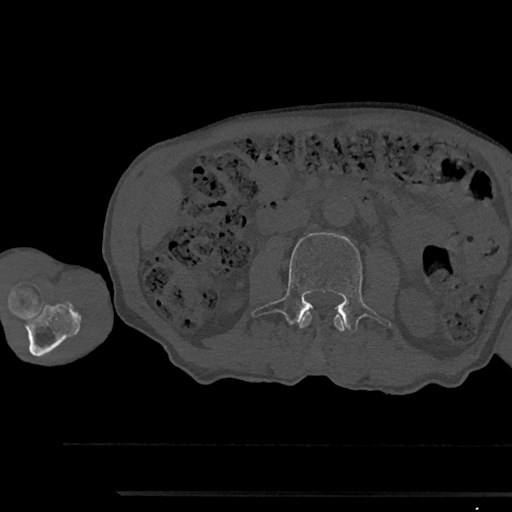
CT including the spine, one axial slice; slice 507 of 797 in the series (ordered by position); reconstruction kernel Br40s/3; bone window (W 1800 / L 400 HU); 0.5 mm slice thickness; 512 × 512 image matrix. Male patient, age 79 years. Case-level facts recorded for this patient, not image findings: primary cancer: prostate.
Structures marked on this image (semi-automatically segmented with operator editing):
- L2 vertebra: bounding box (x1, y1, x2, y2) in pixels: (298, 313, 345, 355)
- L3 vertebra: (252, 233, 392, 330)